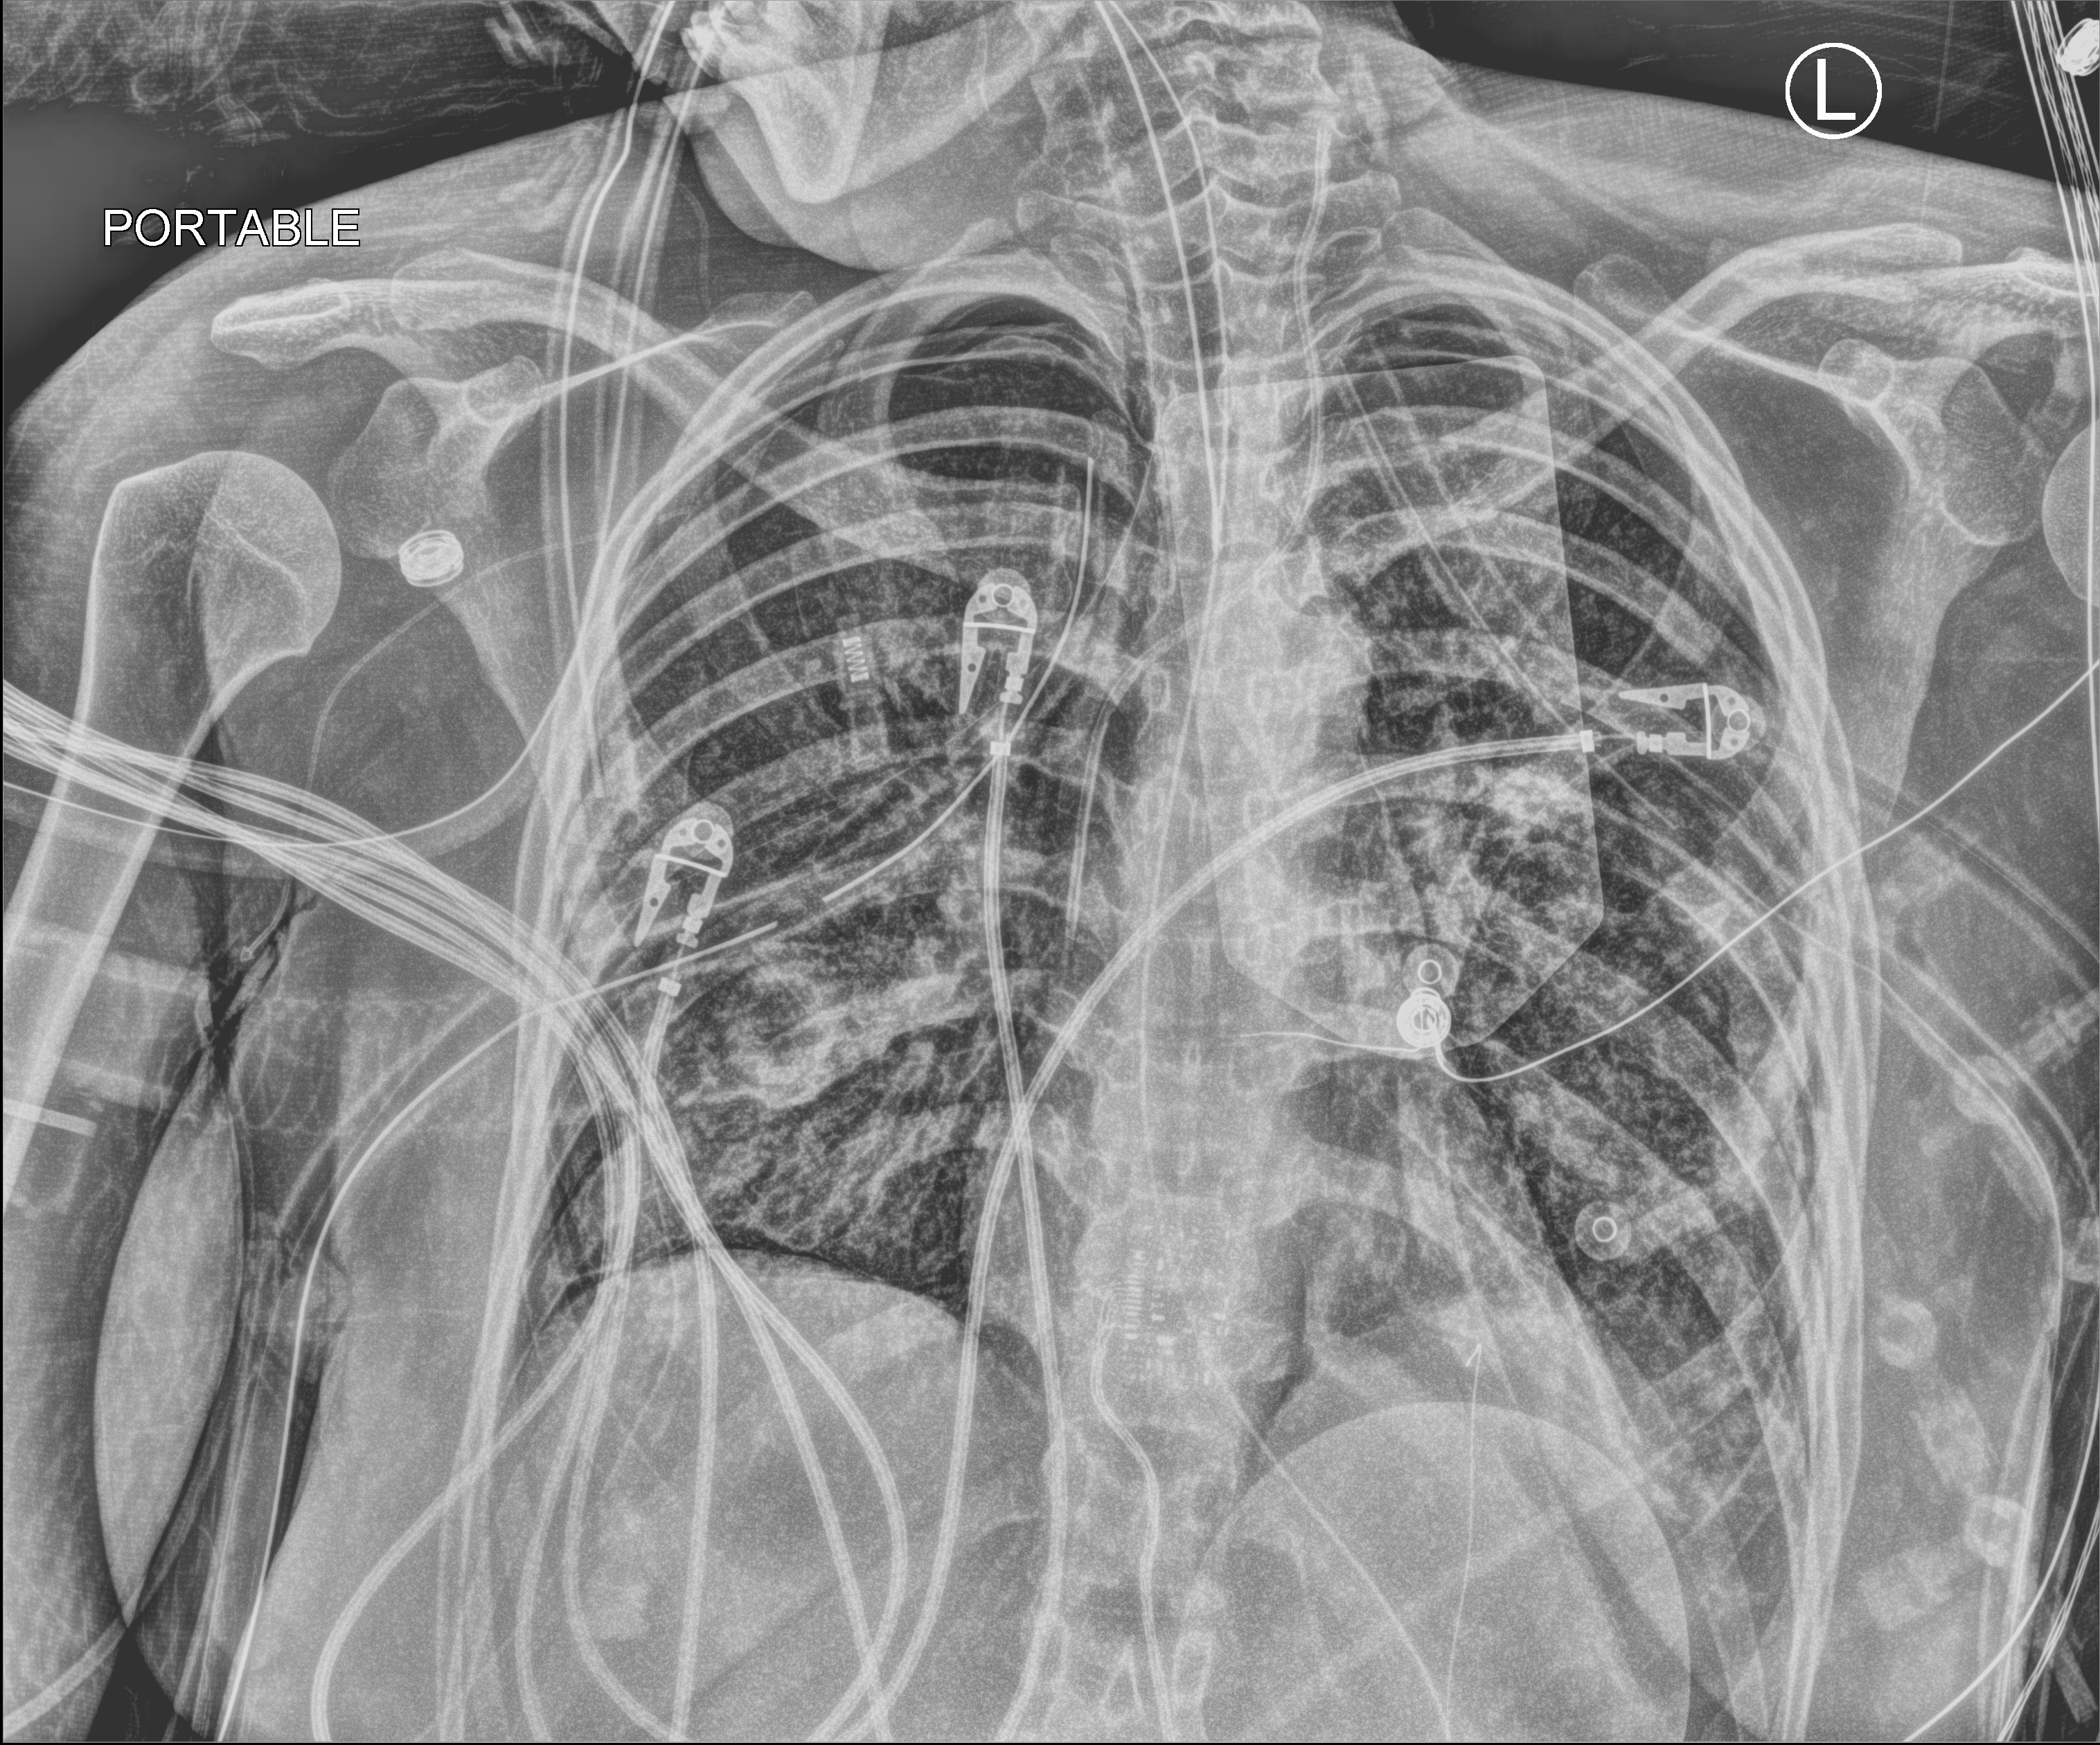
Chest X-ray (portable), anteroposterior (AP) projection. Patient hospitalised with COVID-19, aged 18–59 years.
Admission-level facts for this patient (not findings on this image; timing relative to this image not recorded): mechanically ventilated during this hospital stay: yes; admitted to intensive care during this hospital stay: yes.